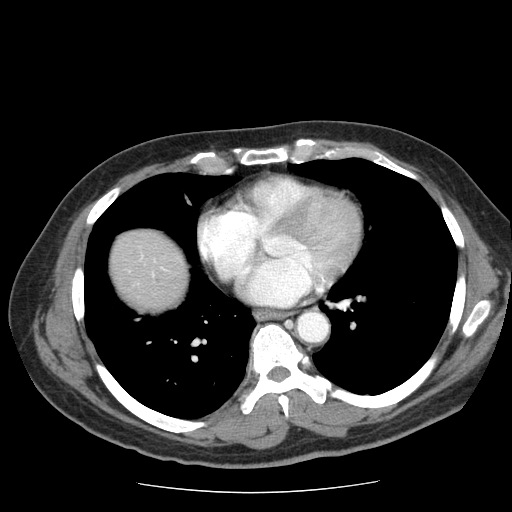
Contrast-enhanced abdominal CT (liver protocol), one axial slice; slice 75 of 85 in the series (ordered by position); reconstruction kernel STANDARD; soft-tissue window (W 400 / L 40 HU); 2.5 mm slice thickness; 512 × 512 image matrix, field of view 360 × 360 mm. From the clinical record (not read from this slice): diagnosis: hepatocellular carcinoma (patient treated with transarterial chemoembolisation; whether this scan precedes or follows treatment is not stated here); TNM stage (as recorded): Stage-IIIA; Child-Pugh class: A; tumour nodularity: multinodular.
Structures marked on this image (semi-automatic segmentation, software-assisted and operator-edited):
- liver parenchyma outside the tumour (the mass and vessels are separate outlines, so this box may not span the whole liver): bounding box <110,228,188,310> (left, top, right, bottom; pixels)